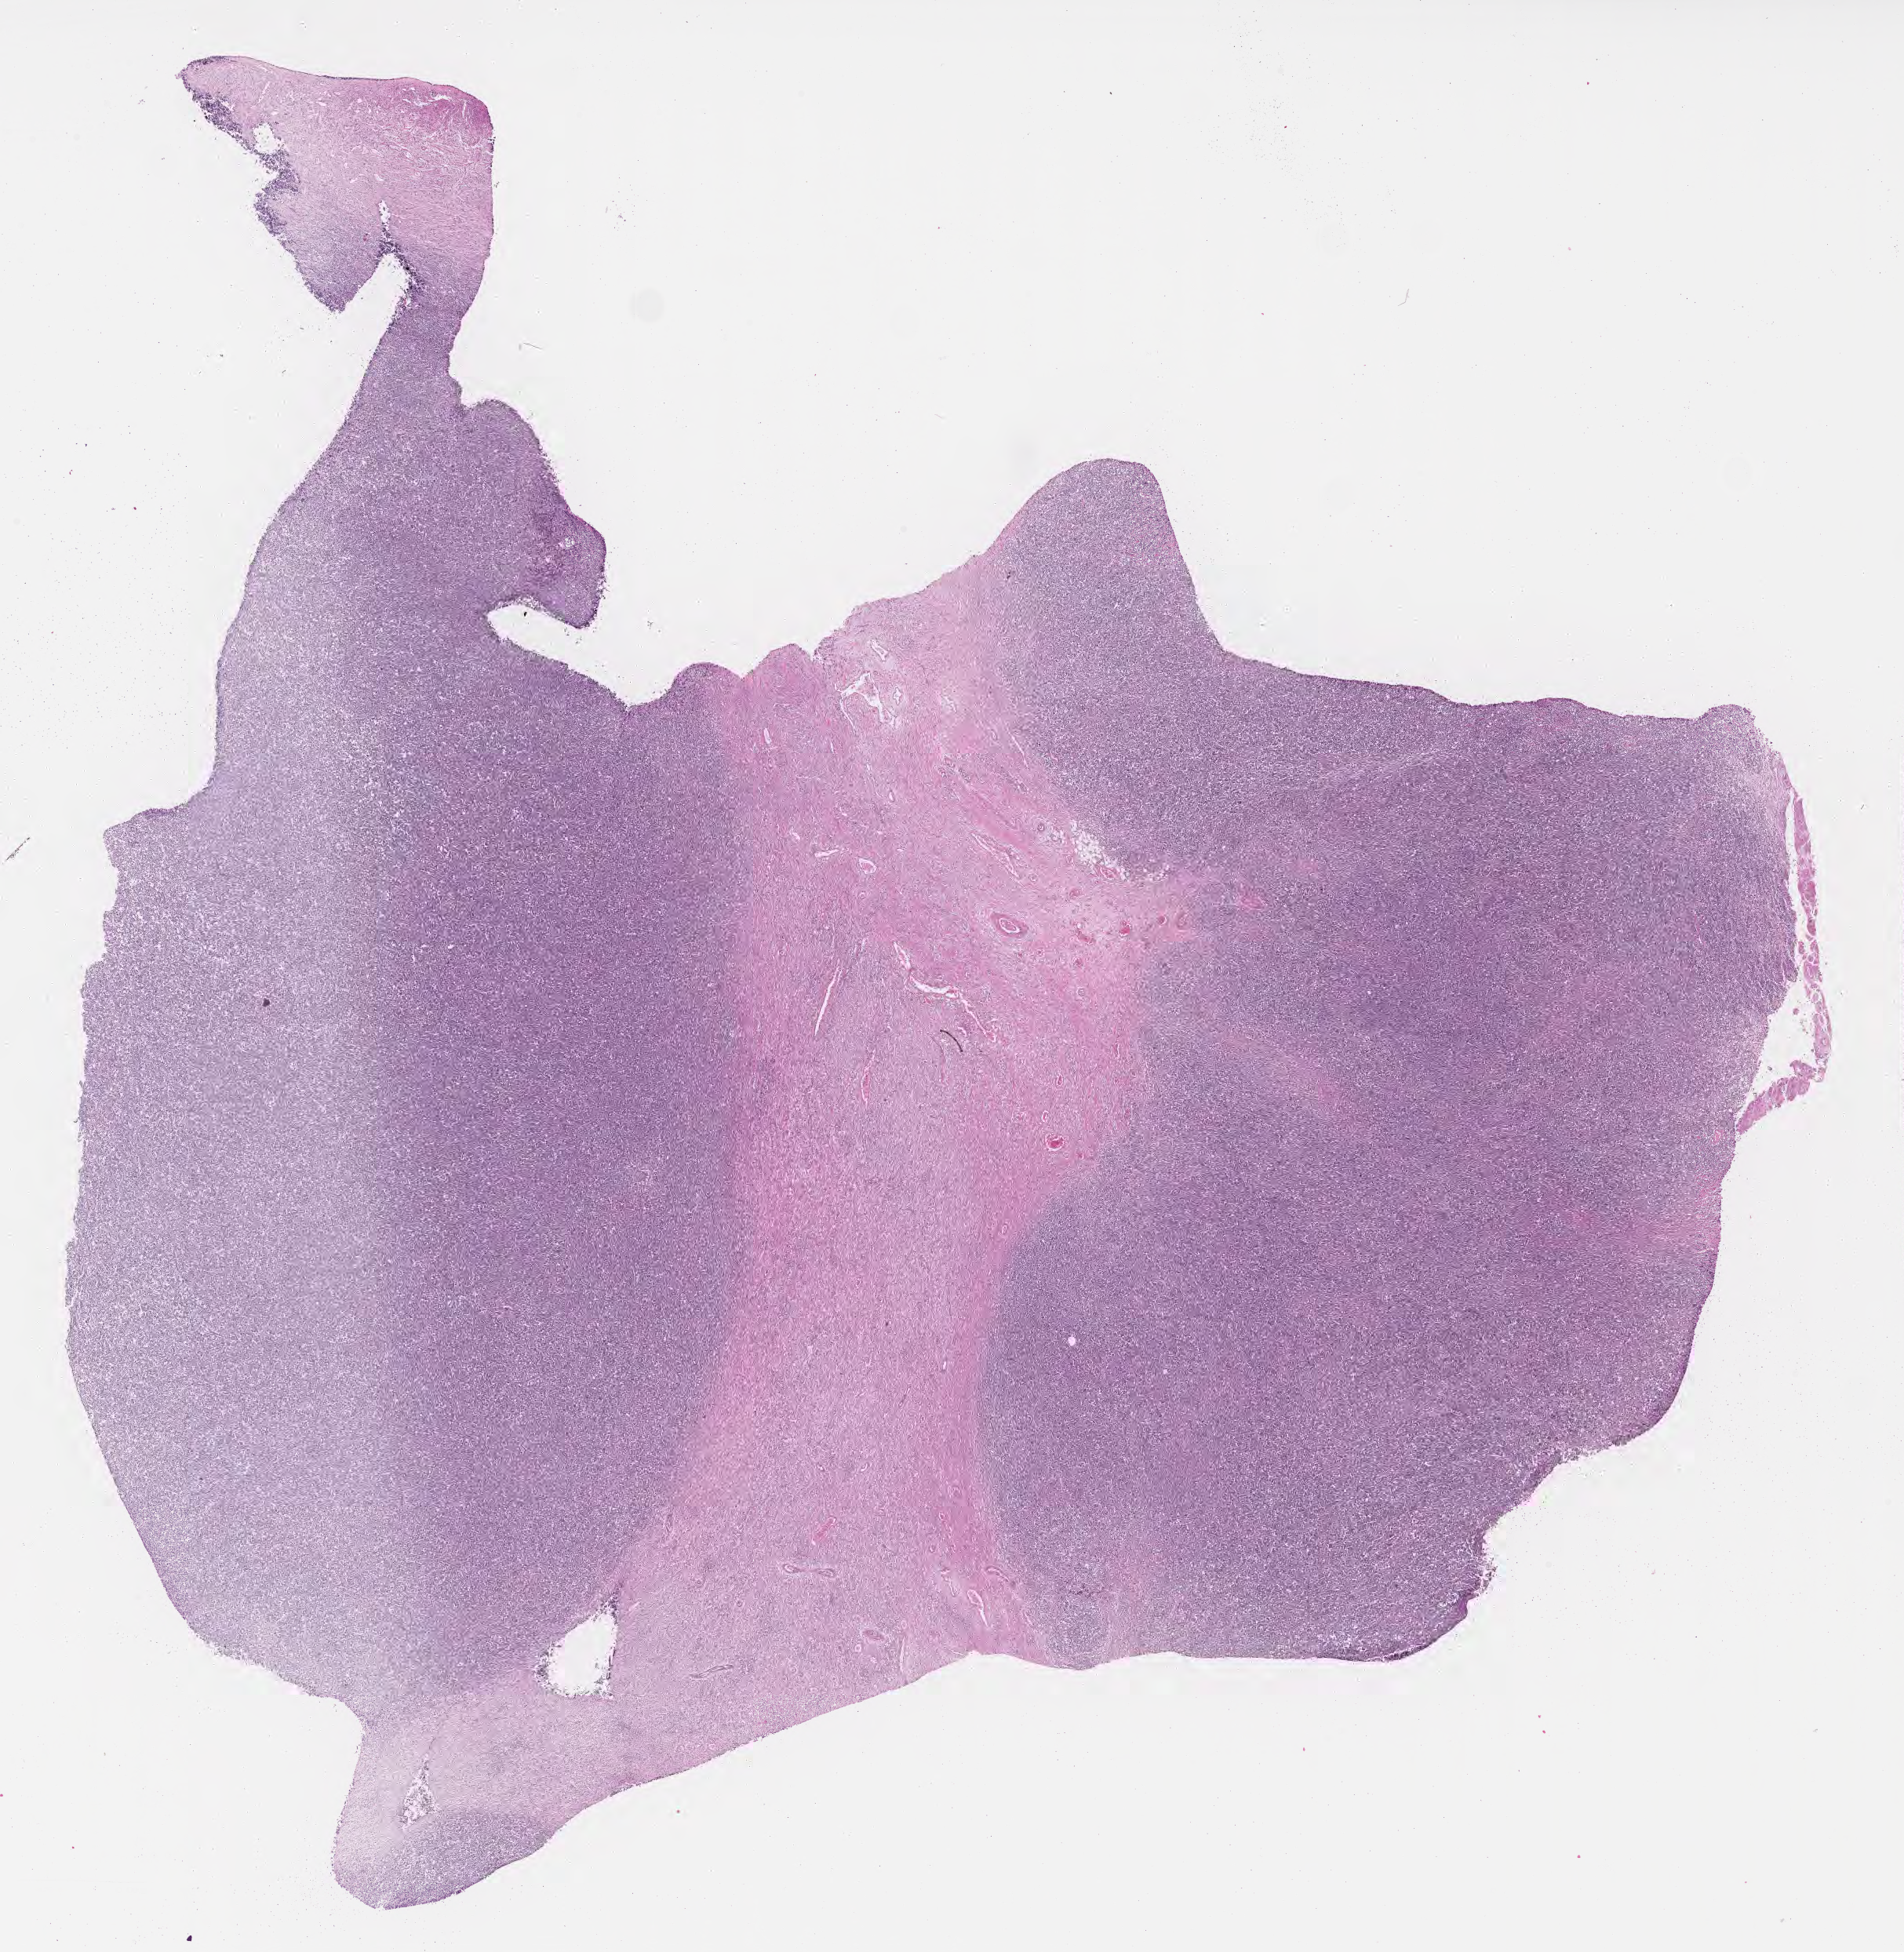
Hematoxylin and eosin (H&E) whole-slide image, shown as a low-resolution overview of the whole scanned area (about 19.6 x 20.1 mm). FFPE section. Primary tumor. Female patient; age at initial diagnosis 8 years. Slide review estimates, as recorded: tumor cells 75%, tumor nuclei 90%, stromal cells 20%, necrosis 5%, normal cells 0%. Infiltration values recorded for this section: lymphocyte infiltration 80%, monocyte infiltration 10%, neutrophil infiltration 0%.
• histologic diagnosis: Burkitt lymphoma, NOS
• Ann Arbor stage (patient): Stage II